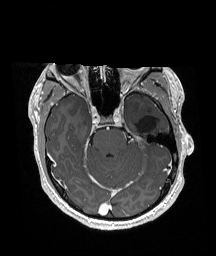
Brain MRI from a brain-tumour surgery series, one axial slice; T1-weighted post-contrast; 1 mm slice thickness; 216 × 256 image matrix, field of view 211 × 250 mm. From the clinical record (not read from this slice): histopathology: Glioneuronal tumor; WHO grade: 2; tumour location: Left Superior Temporal Gyrus.
Structures marked on this image (manually delineated by an expert):
- previous resection cavity: bounding box (x1, y1, x2, y2) in pixels: (137, 115, 159, 136)